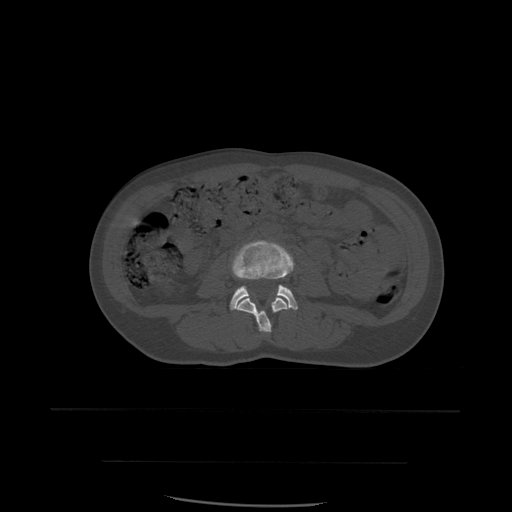
CT including the spine, one axial slice. Slice 184 of 574 in the series (ordered by position). Bone window (W 1800 / L 400 HU). 512 × 512 image matrix, field of view 392 × 392 mm. Patient age 48 years. Case-level facts recorded for this patient, not image findings: primary cancer: lung.
Annotated regions visible in this slice (semi-automatically segmented with operator editing):
- L3 vertebra: box from (x=236, y=298) to (x=288, y=333) px
- L4 vertebra: (x=230, y=241)–(x=298, y=310)